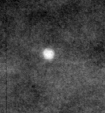
Cropped region of a digitized screen-film mammogram centred on a radiologist-marked abnormality, right breast, CC view, BI-RADS breast density category 3 (scale 1–4).
Marked abnormality: calcifications, morphology round and regular / lucent center; BI-RADS assessment category 2; benign without callback (not worked up further).